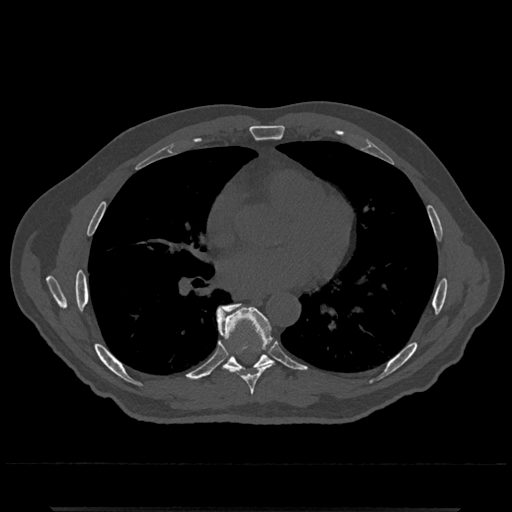
CT including the spine, one axial slice. Slice 698 of 797 in the series (ordered by position). Reconstruction kernel Br40s/3. 120 kVp. Bone window (W 1800 / L 400 HU). 0.5 mm slice thickness. 512 × 512 image matrix, field of view 393 × 393 mm. Male patient, age 67 years. Case-level facts recorded for this patient, not image findings: primary cancer: prostate.
Structures marked on this image (semi-automatic segmentation, software-assisted and operator-edited):
- T7 vertebra: bounding box (x1, y1, x2, y2) in pixels: (217, 308, 274, 395)
- T8 vertebra: (216, 303, 272, 372)